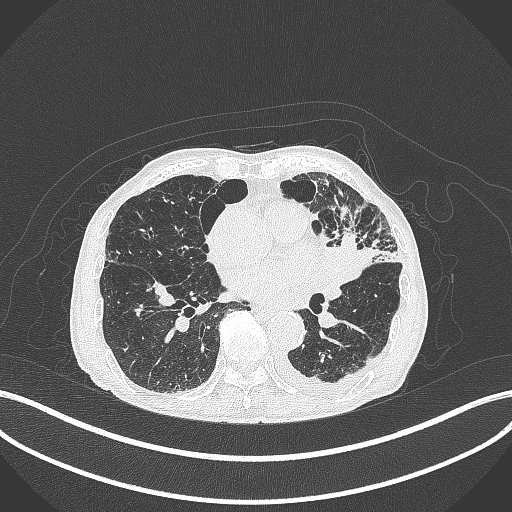
Chest CT, one axial slice; position 171 of 385 along the scan axis; lung window (W 1500 / L -600 HU); 512 × 512 image matrix, field of view 400 × 400 mm. Patient: male, 90 years or older. From the clinical record (not read from this slice): clinical TNM (as recorded): T2b N1 M0.
Structures marked on this image (bounding box drawn by a radiologist):
- lung tumour (recorded histology: squamous cell carcinoma): bounding box <318,233,382,289> (left, top, right, bottom; pixels)